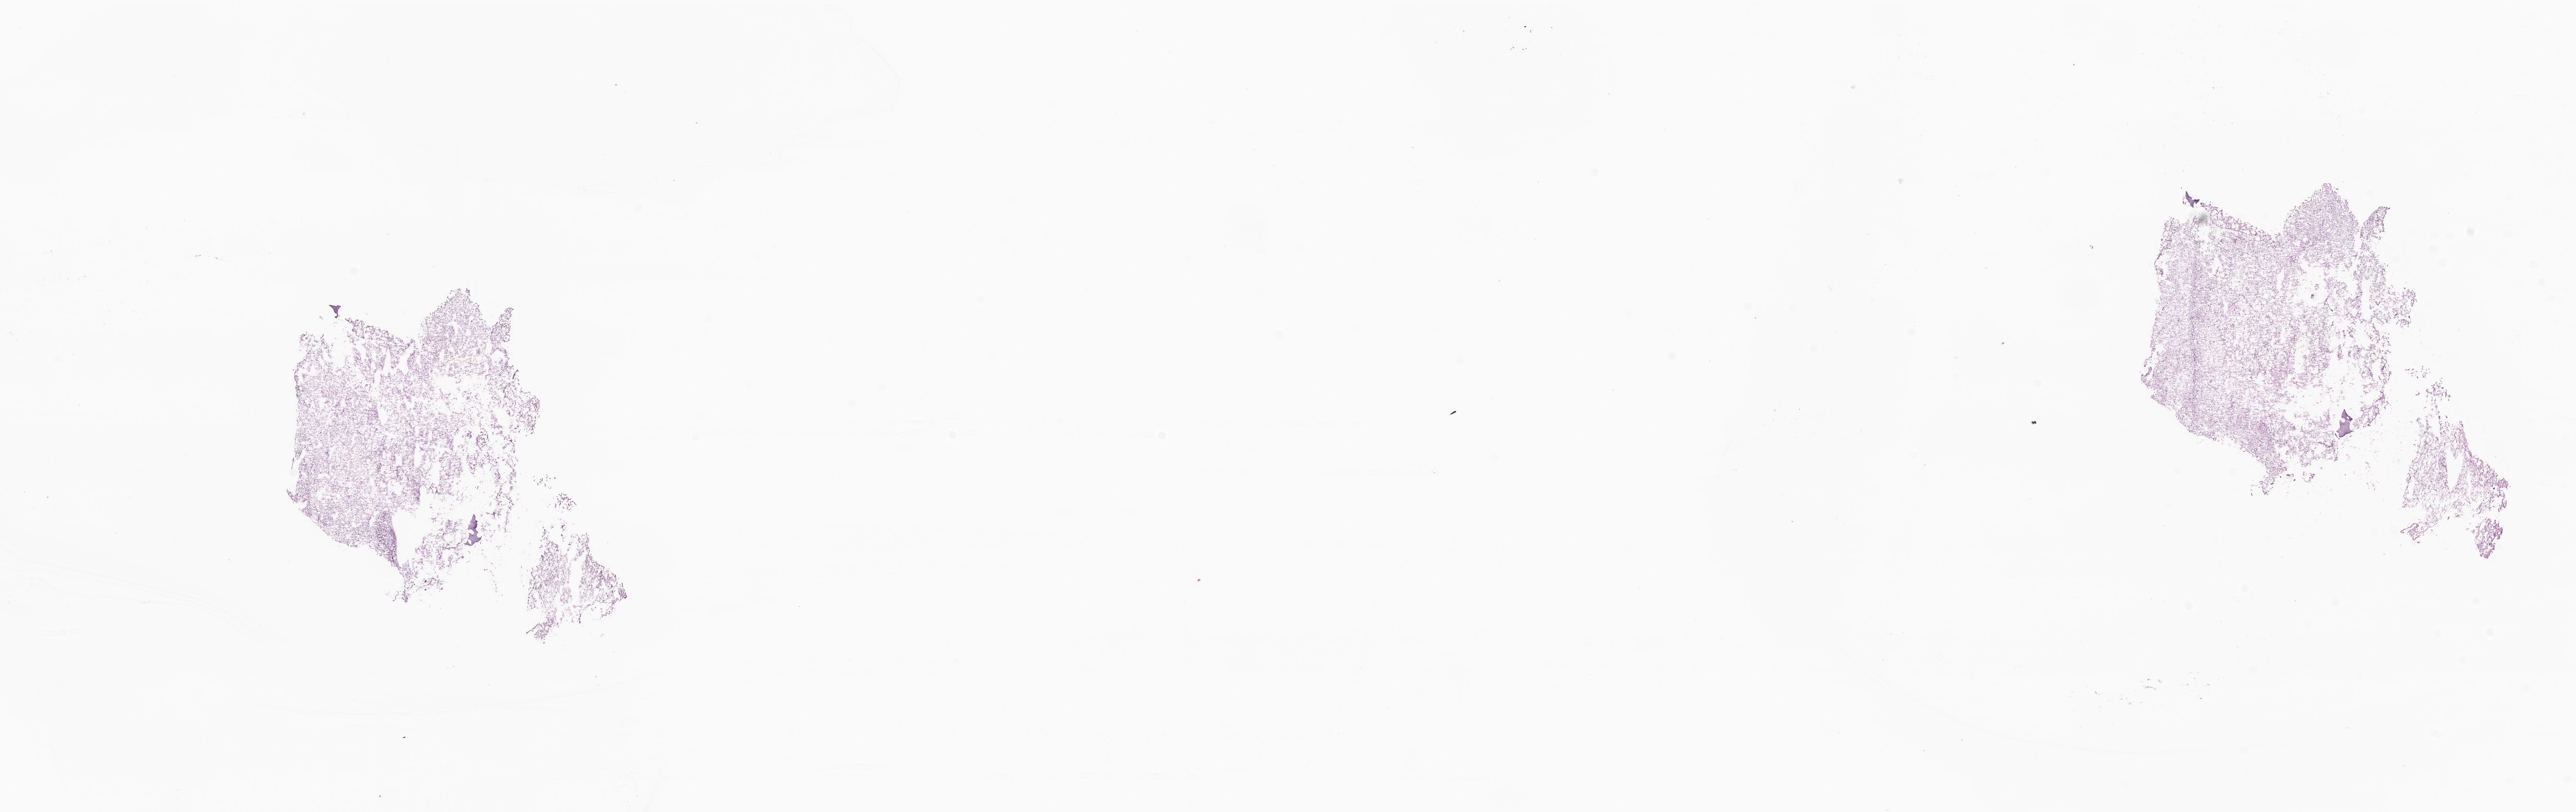
Haematoxylin and eosin whole-slide image of tumor tissue from the cerebellum — whole scanned area (about 28.1 x 8.9 mm) shown as a low-resolution overview; frozen section (OCT-embedded). Patient: female, age 49 months (4 years 1 month).
Recorded diagnosis: Pilocytic astrocytoma.